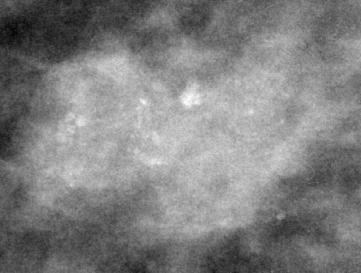
Region of interest cut from a scanned film mammogram (one marked finding); right breast; CC view.
Marked abnormality: calcifications, morphology pleomorphic, distribution clustered; BI-RADS assessment category 4; pathology (as recorded): malignant.